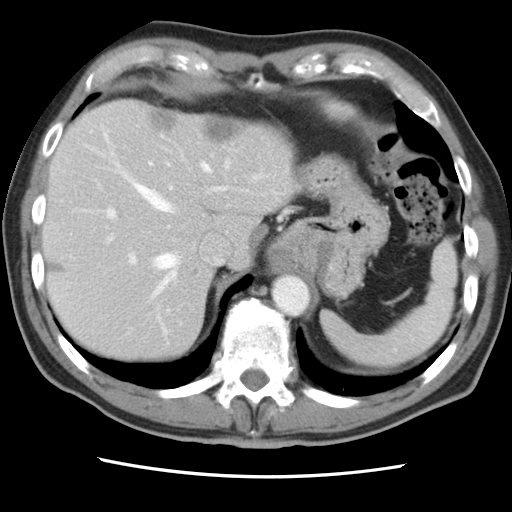
Contrast-enhanced abdominal CT, one axial slice; position 65 of 83 along the scan axis; intravenous contrast given; soft-tissue window (W 400 / L 40 HU); 5 mm slice thickness; 512 × 512 image matrix. Male patient, age 69 years. From the clinical record (not read from this slice): diagnosis: colorectal cancer liver metastases, imaged before liver resection; multiple liver metastases: yes.
Annotated regions visible in this slice (expert manual segmentation):
- hepatic veins: bounding box [x1, y1, x2, y2] px = [85, 128, 212, 331]
- liver: [44, 100, 291, 360]
- planned liver remnant (the part of the liver to remain after resection): [44, 145, 212, 360]
- portal vein (with intrahepatic branches): [106, 161, 173, 264]
- liver metastasis: [152, 113, 178, 130]
- liver metastasis: [191, 270, 199, 276]
- liver metastasis: [204, 121, 241, 142]